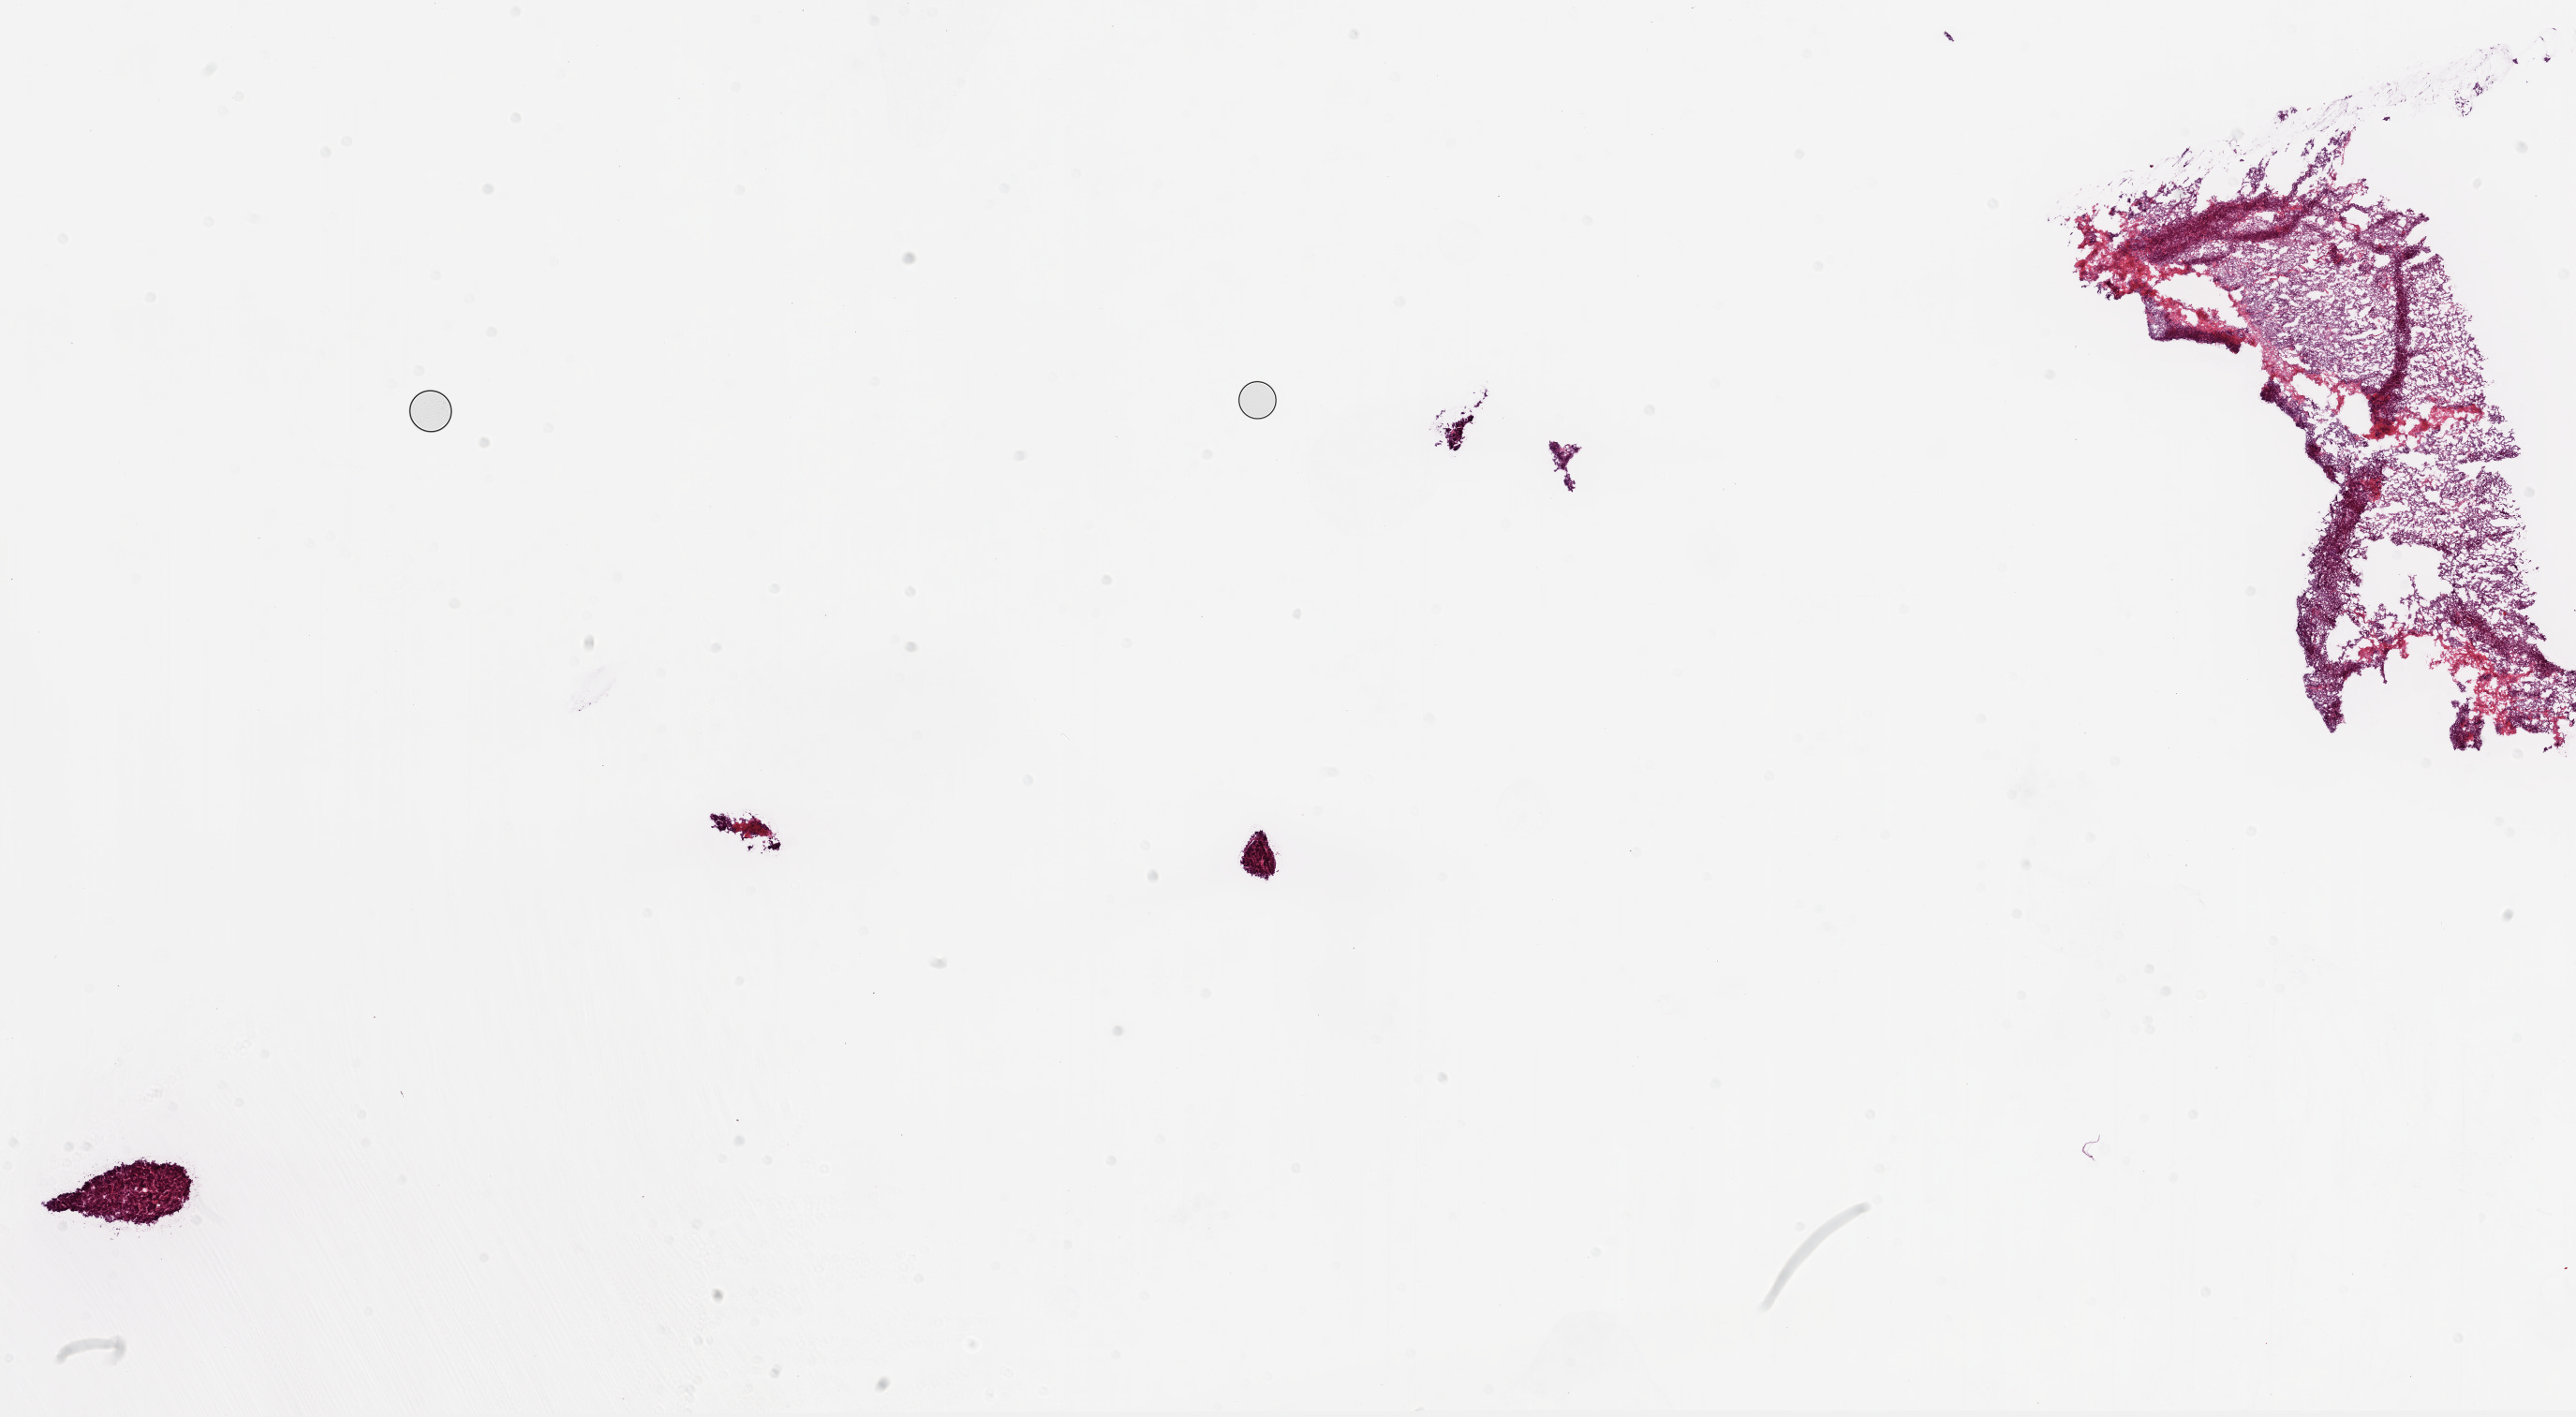
Digitized H&E tissue section (whole slide), shown as a low-resolution overview of the whole scanned area (about 22.1 x 12.1 mm), frozen section from the top of the tissue portion, sample: primary tumour, ovary. Female, age 49 years at initial diagnosis. Histologic grade: G2 (moderately differentiated). Composition of this section per pathologist review: tumour cells 95%, tumour nuclei 99%, normal cells 0%, stromal cells 2%, necrosis 3%.
FIGO stage: IIIB. Pathologic diagnosis: Serous cystadenocarcinoma, NOS.